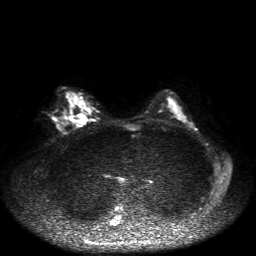
Breast MRI, one axial slice; slice 28 of 50 in the series (ordered by position); diffusion-weighted series; image 2 of 4 stored at this slice position (different b-values; order by instance number); 1.5 T; 4 mm slice thickness; 256 × 256 image matrix. Female patient.
Annotated regions visible in this slice (expert manual segmentation):
- tumour on diffusion-weighted imaging: bounding box <70,114,87,123> (left, top, right, bottom; pixels)